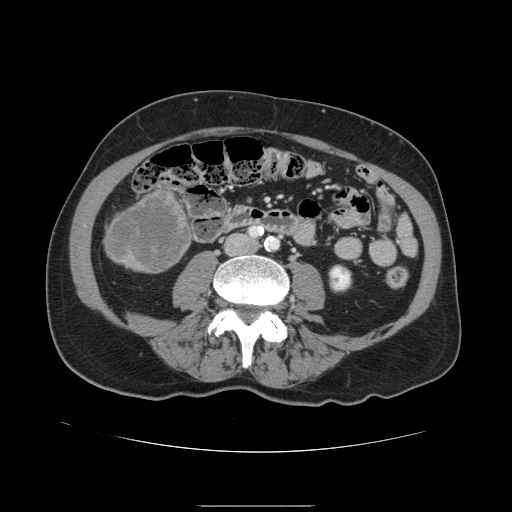
Contrast-enhanced abdominal CT, one axial slice; position 20 of 168 along the scan axis; intravenous contrast given; soft-tissue window (W 400 / L 40 HU); 512 × 512 image matrix, field of view 386 × 386 mm. Male patient, age 74 years. Case-level facts recorded for this patient, not image findings: diagnosis: colorectal cancer liver metastases, imaged before liver resection; multiple liver metastases: no; largest metastasis: 14.5 cm; disease in both lobes: yes.
Structures marked on this image (expert manual segmentation):
- liver: bounding box <105,186,193,274> (left, top, right, bottom; pixels)
- liver metastasis: <109,192,190,272>